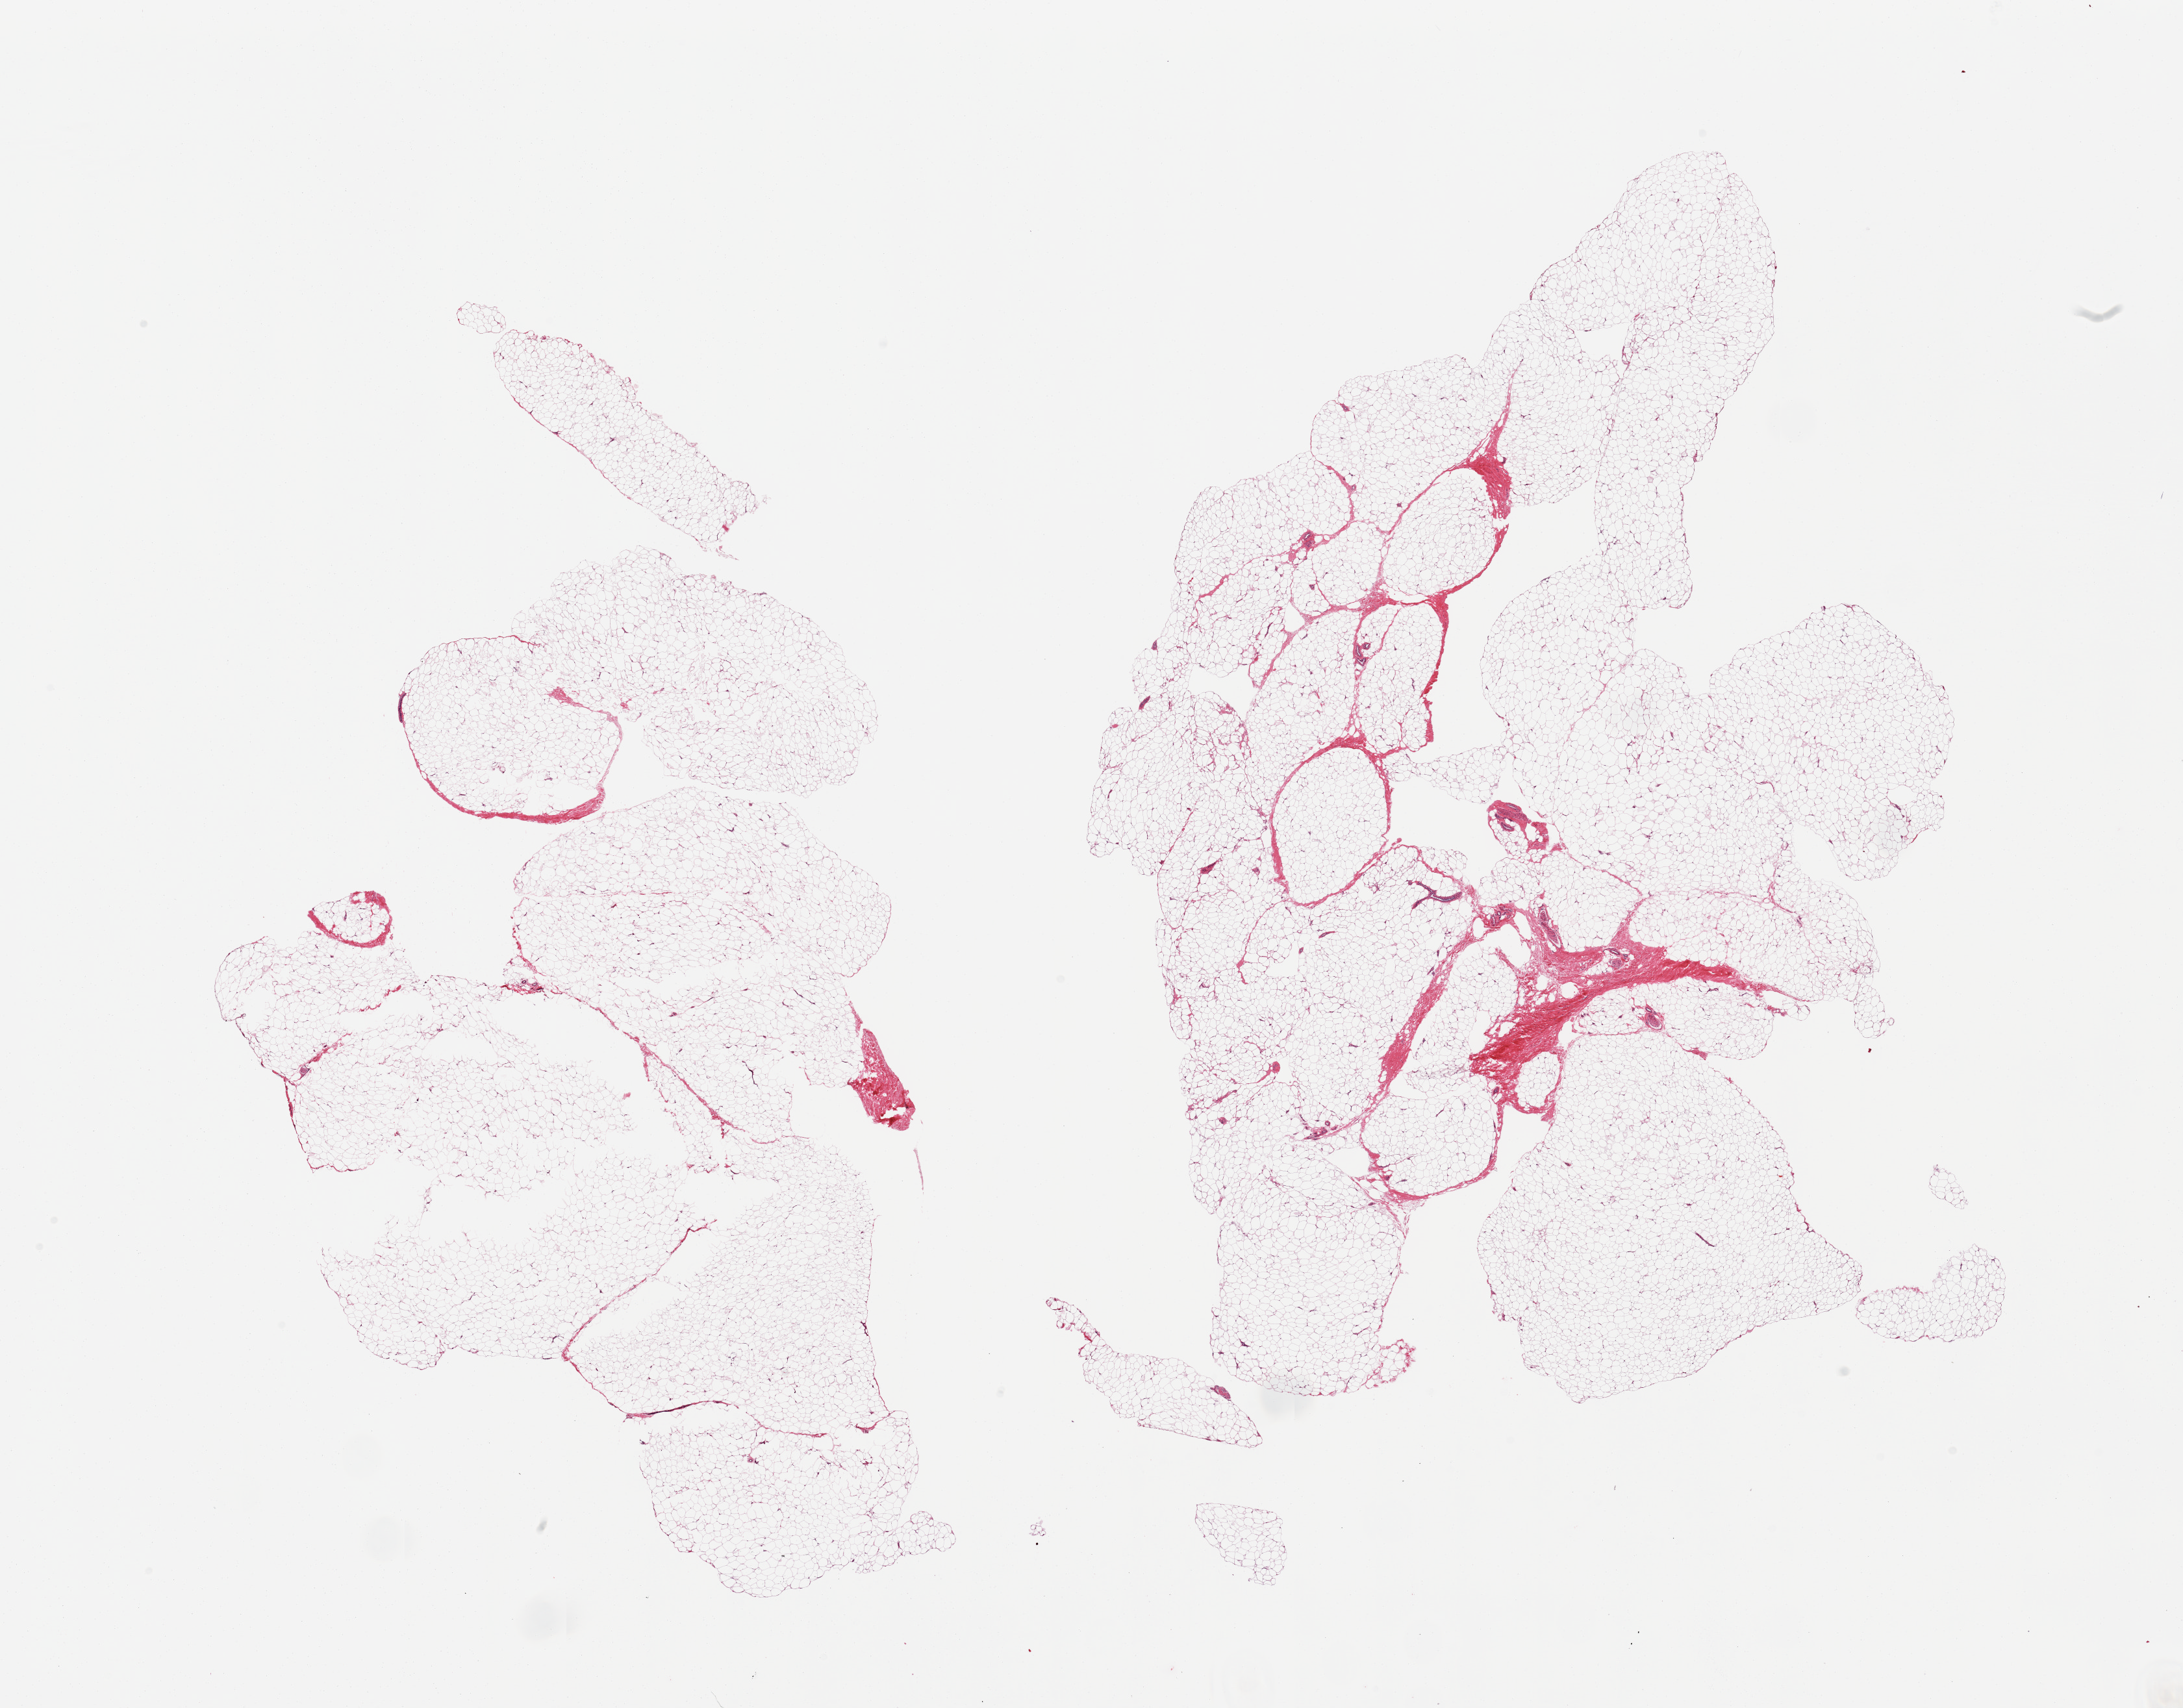
Whole-slide image, H&E stain, shown as a low-resolution overview of the whole scanned area (about 26.6 x 20.8 mm). PAXgene-fixed, paraffin-embedded tissue. Sampled site (target tissue): adipose tissue. Tissue donor sample. Donor sex: male.
Pathologist's review note for this sample: 2 pieces.